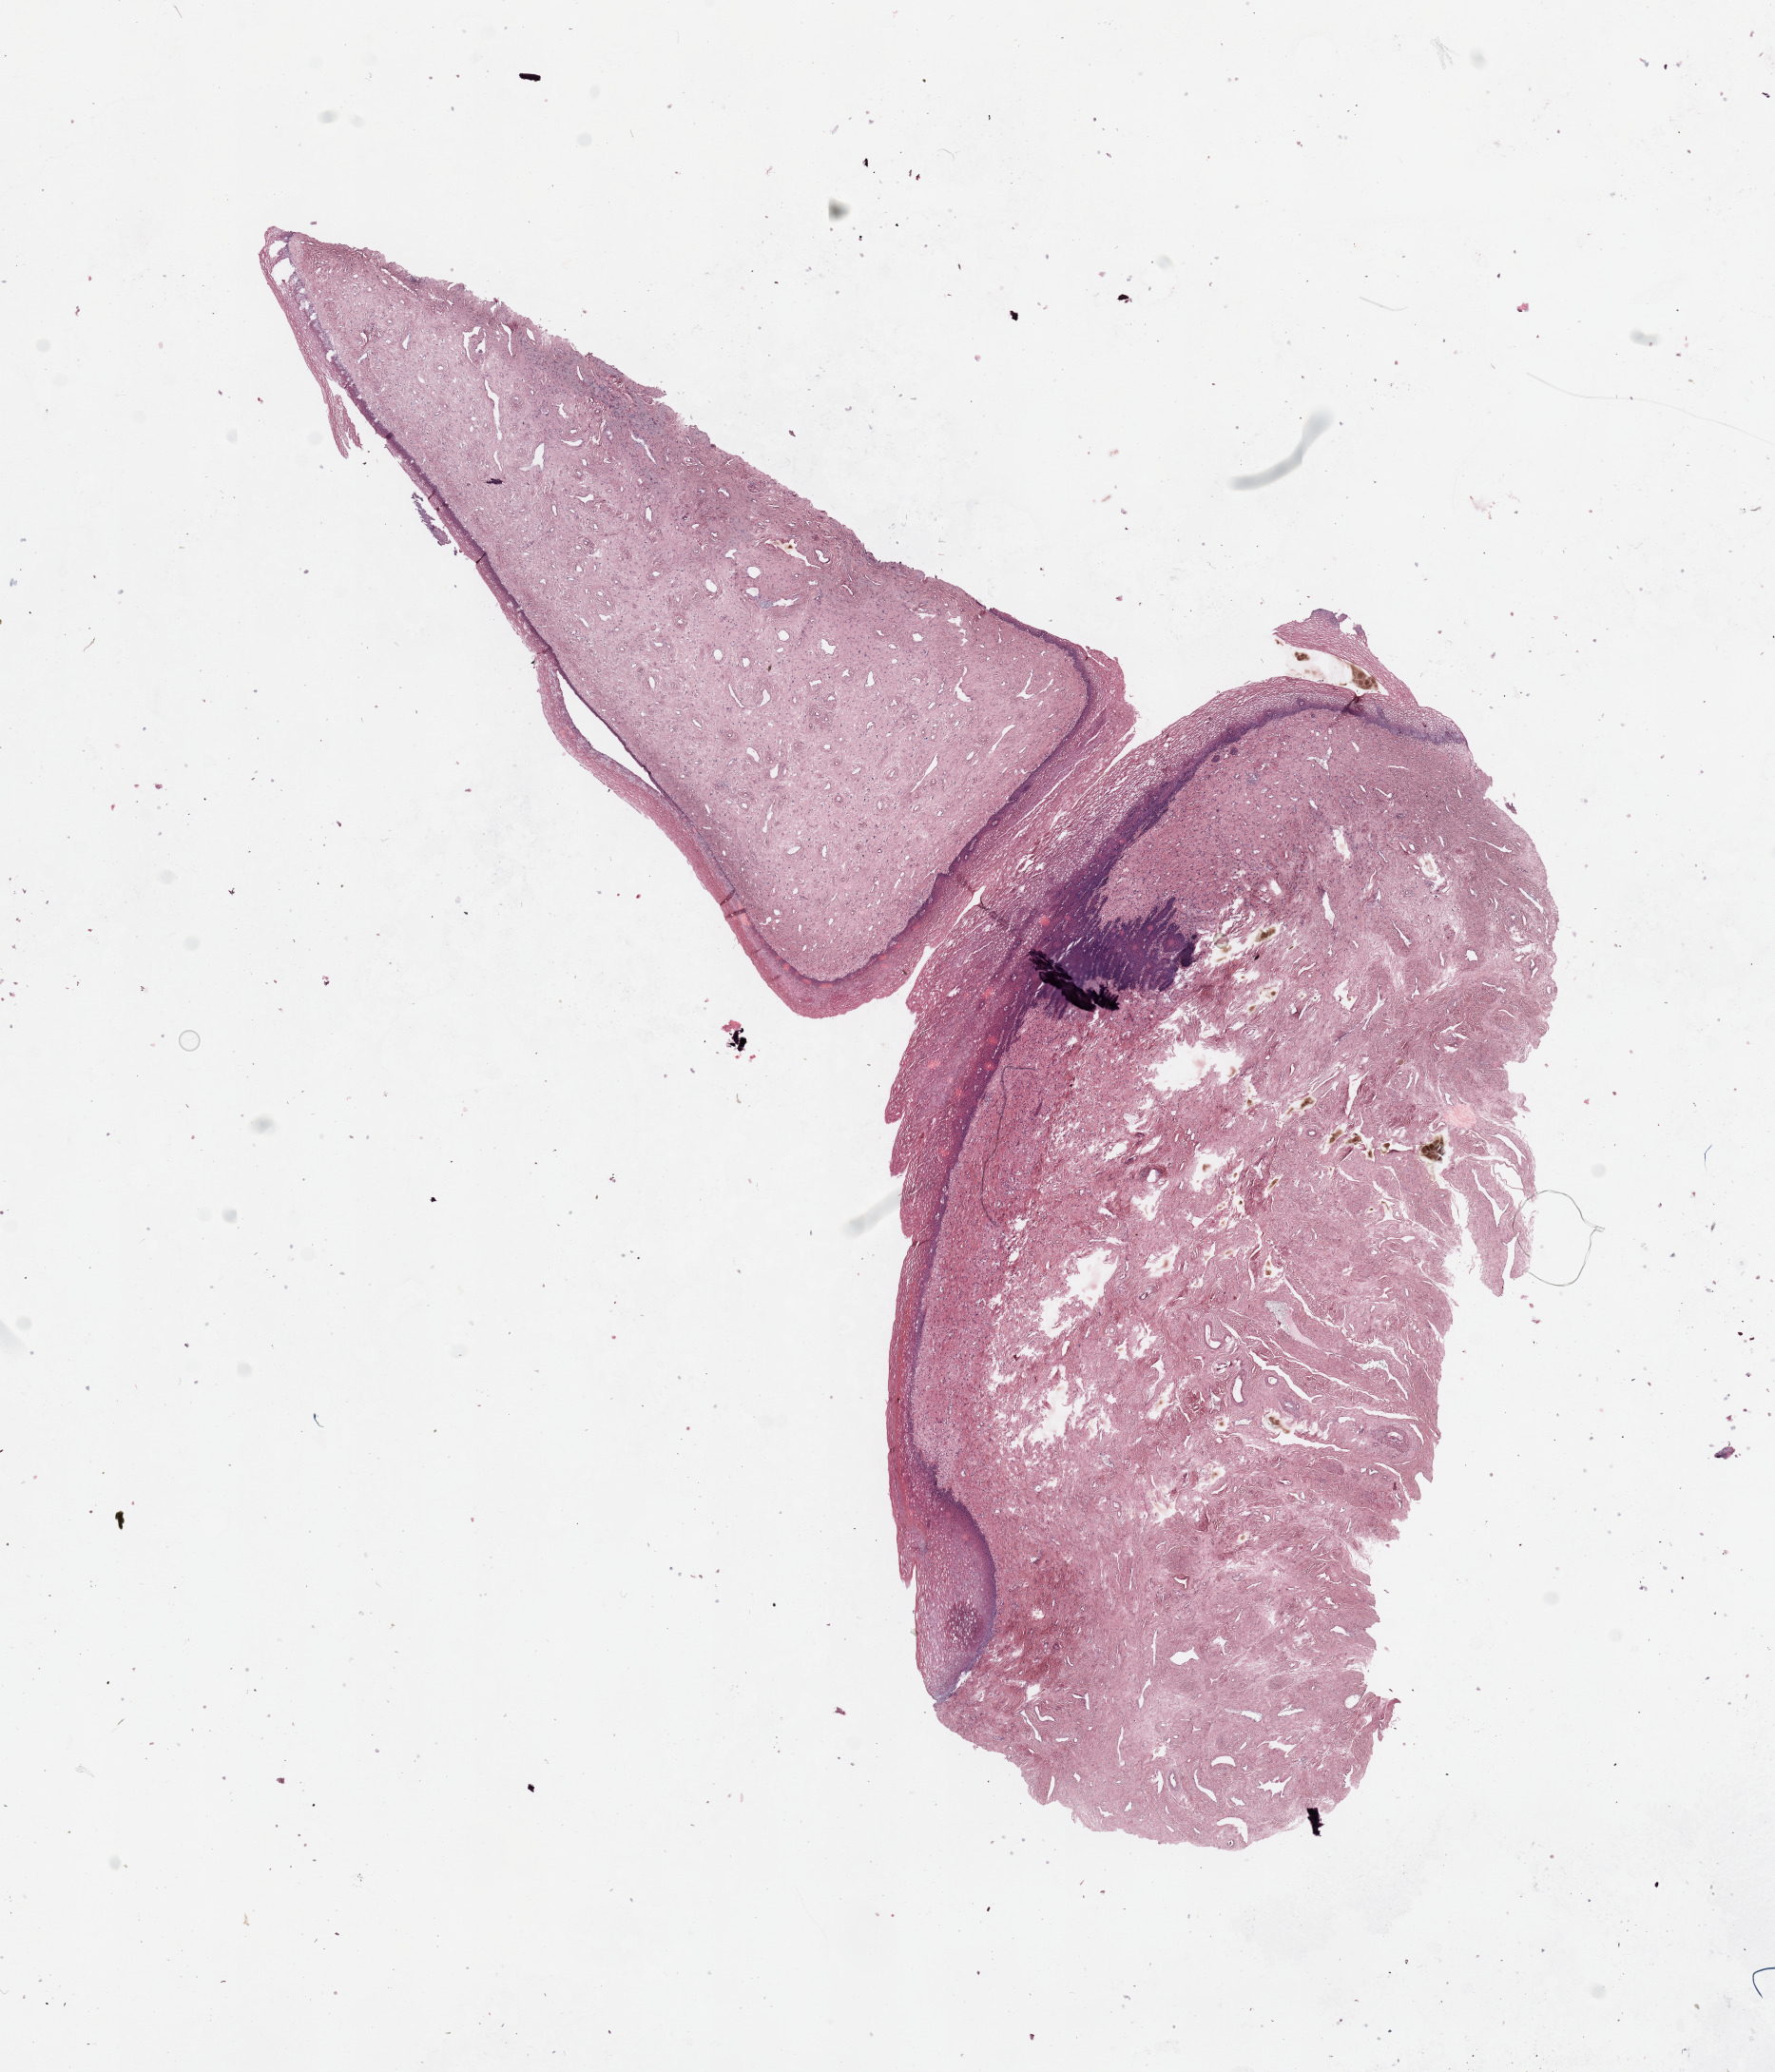
Hematoxylin and eosin (H&E) stained whole-slide image — whole scanned area (about 14.8 x 17.2 mm, from a 20x scan) shown as a low-resolution overview; uterus, normal (non-tumour) tissue. 62-year-old female patient.
This section: normal (non-tumour) tissue from the same patient. Patient diagnosis: Endometrioid adenocarcinoma, NOS.